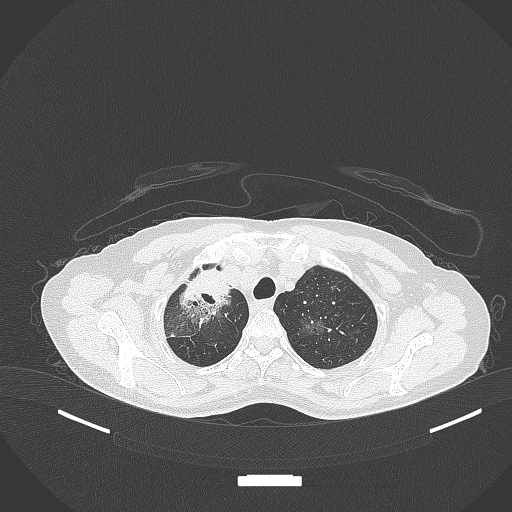
Chest CT, one axial slice. Position 275 of 284 along the scan axis. Reconstruction kernel B70f. 120 kVp. Lung window (W 1500 / L -600 HU). 1 mm slice thickness. 512 × 512 image matrix. Patient: female, 59 years. Case-level facts recorded for this patient, not image findings: clinical TNM (as recorded): T3 N0 M0; histopathological grade: G1.
Structures marked on this image (rectangle marked by the reading radiologist):
- lung tumour (recorded histology: adenocarcinoma): bounding box <175,261,230,326> (left, top, right, bottom; pixels)